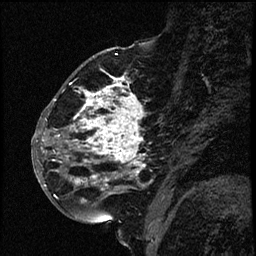
Breast MRI (dynamic contrast-enhanced), one sagittal slice. Position 29 of 66 along the scan axis. Dynamic contrast-enhanced study with each time point stored as its own series, time point 2 of 3 at this slice position (early post-contrast, ordered by acquisition time). 1.5 T. TE 4.2 ms, TR 17.6 ms. 2 mm slice thickness. 256 × 256 image matrix, field of view 200 × 200 mm. Female patient. From the clinical record (not read from this slice): setting: breast cancer imaged before/during neoadjuvant chemotherapy; receptor status: HER2-positive.
Outlined on this slice (semi-automatic segmentation, software-assisted and operator-edited):
- analysis volume of interest (the breast-tissue region the enhancement analysis was run in; not a lesion): bounding box (x1, y1, x2, y2) in pixels: (52, 69, 165, 209)
- tumour enhancement mask (voxels above the 100 % enhancement threshold inside the analysis volume of interest): (53, 77, 146, 195)